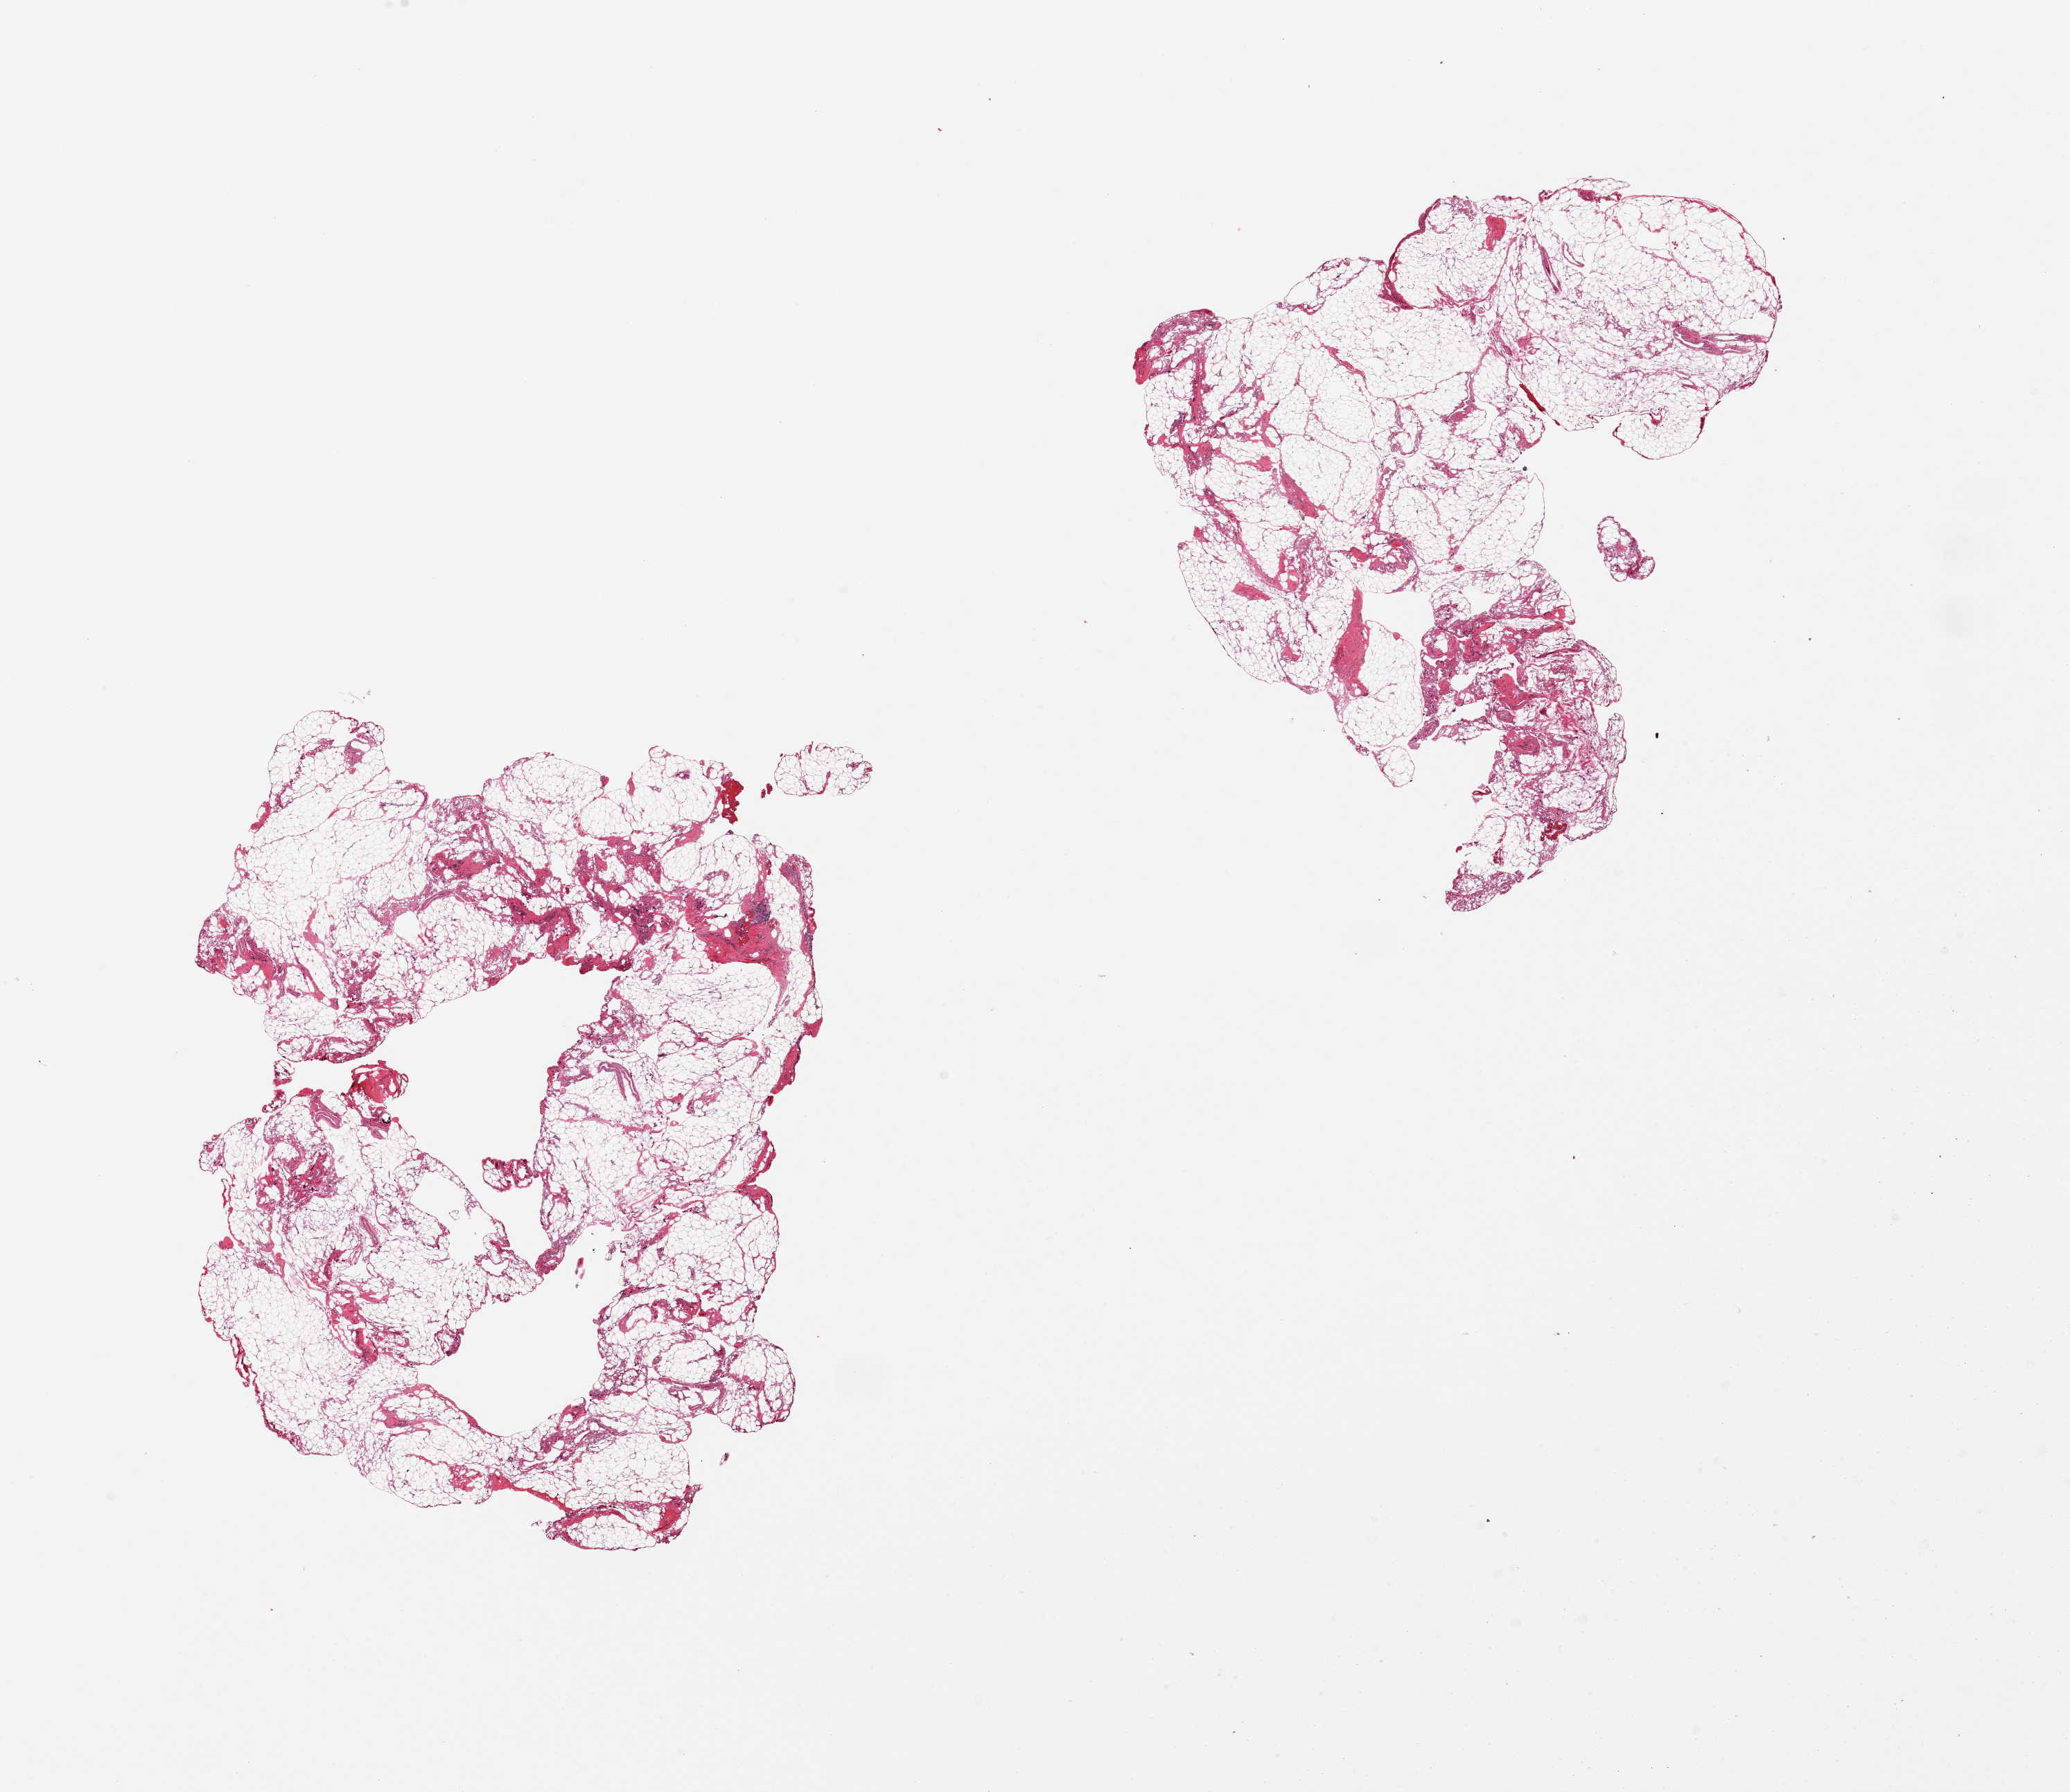
Whole-slide image, haematoxylin and eosin stain — a low-resolution overview of the entire scanned area, about 23.6 x 20.5 mm (acquisition: 20x scan); PAXgene-fixed paraffin-embedded (PFPE) section; section of omentum (target tissue); tissue donor sample. Donor: female.
Reviewer comment on this tissue sample: 2 pieces, abundant small vessels intimately intermingled with fat.